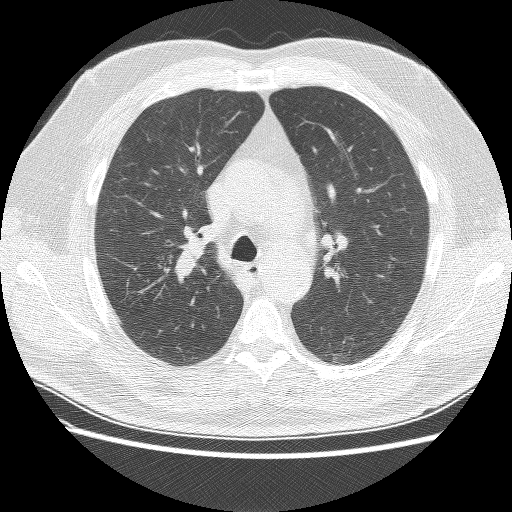
Low-dose screening chest CT, axial slice; baseline screening round; lung window (W 1500 / L -600 HU); 2.5 mm slice thickness; lung (sharp) reconstruction kernel (BONE); 120 kVp; slice 61 of 159 in the series; 512 × 512 image matrix. Male participant, aged 57 years at enrolment.
Expert reader's lesion annotation, bounding box (x1, y1, x2, y2) in pixels: (157, 240, 213, 293). No non-calcified nodule or mass ≥4 mm was recorded by the screening reader at this exam. Official screen result: negative screen, minor abnormalities not suspicious for lung cancer.